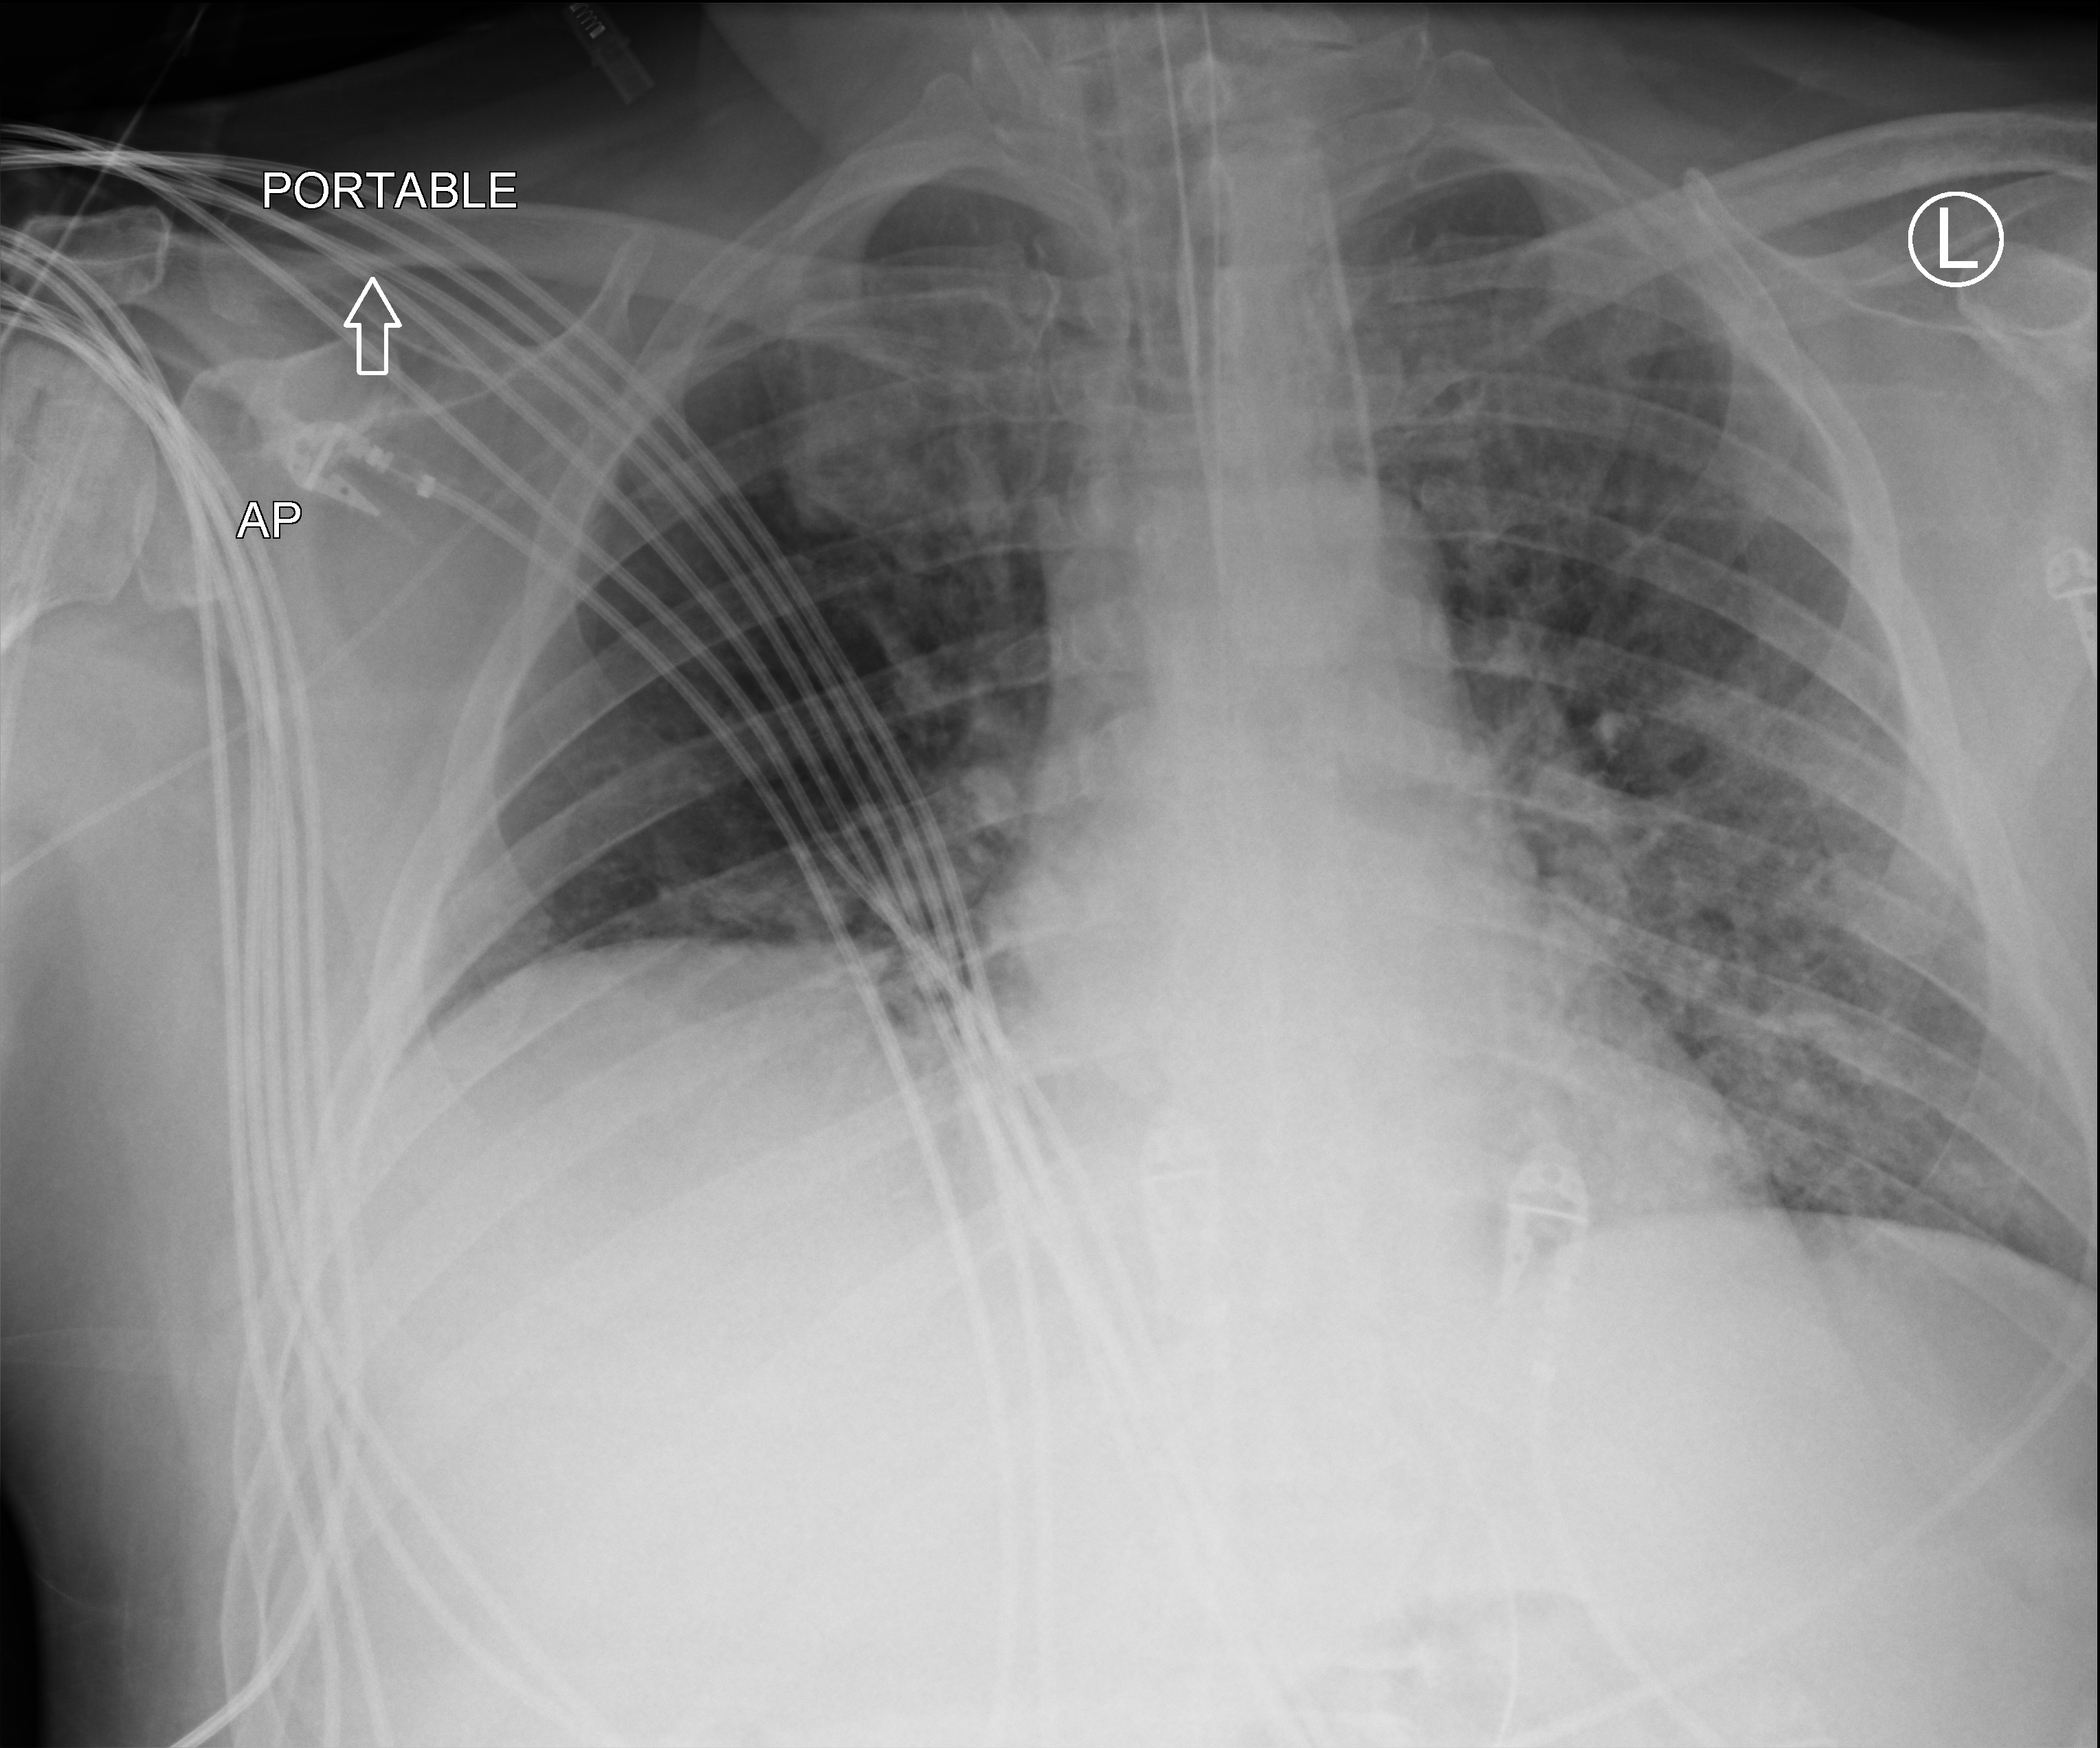
Bedside chest radiograph (computed radiography); anteroposterior (AP) projection. Patient hospitalised with COVID-19; male, aged 18–59 years.
Admission-level facts for this patient (not findings on this image; timing relative to this image not recorded): admitted to intensive care during this hospital stay: yes.